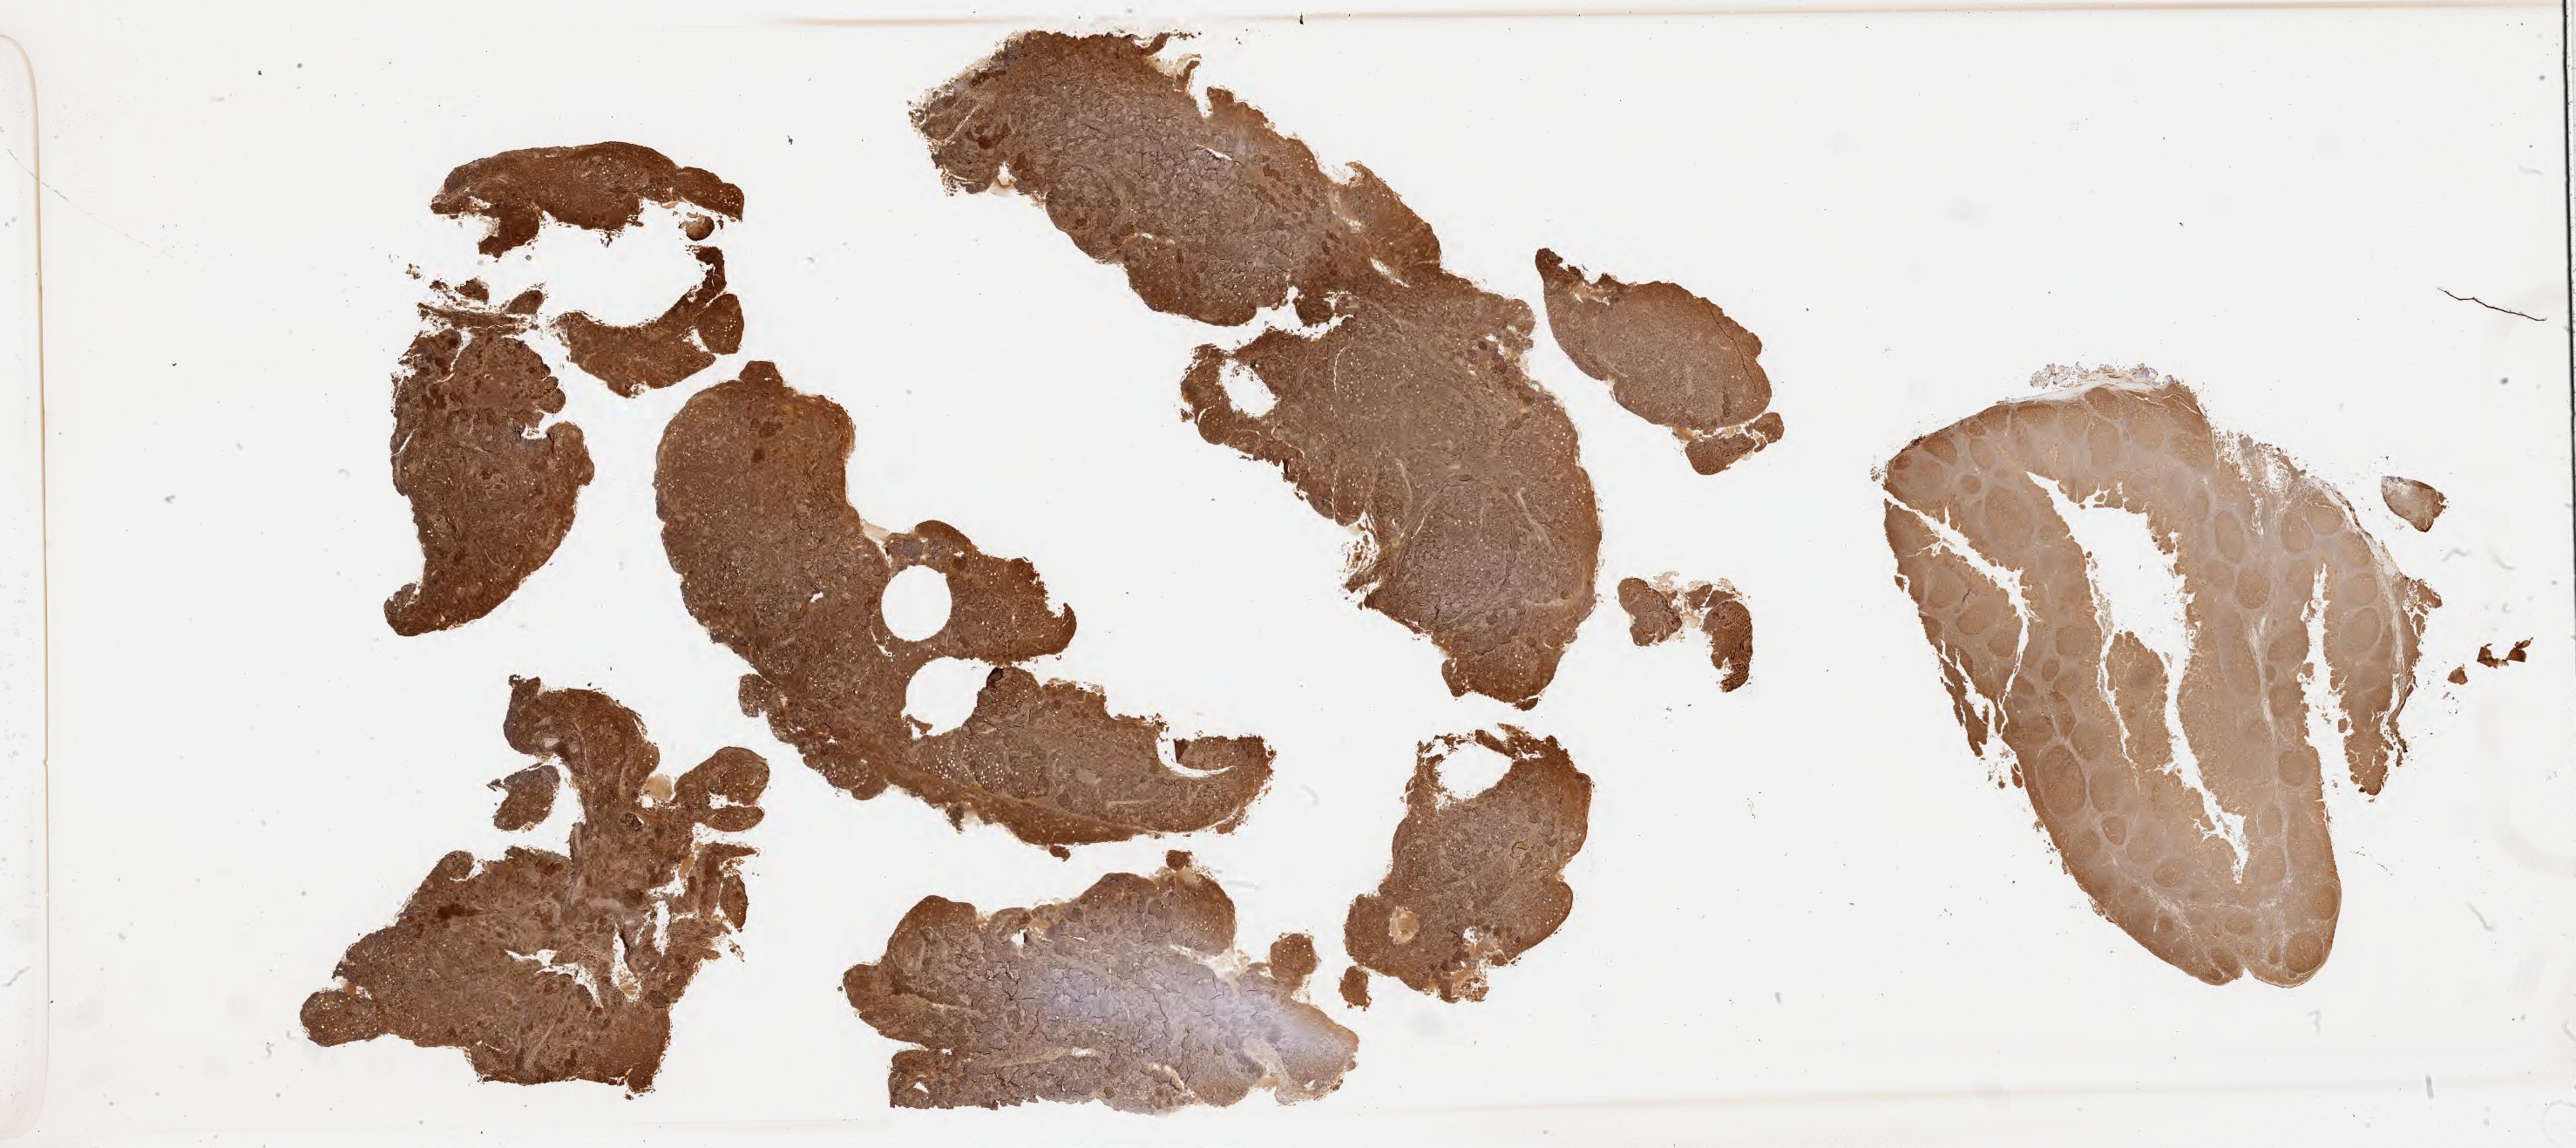
Immunohistochemistry (IHC) whole-slide image stained for BCL6, whole scanned area (about 47.8 x 21.3 mm) shown as a low-resolution overview, specimen: tumor tissue, site: cranium. Patient: male, age at initial diagnosis 5 years.
* histologic diagnosis: Burkitt lymphoma, NOS